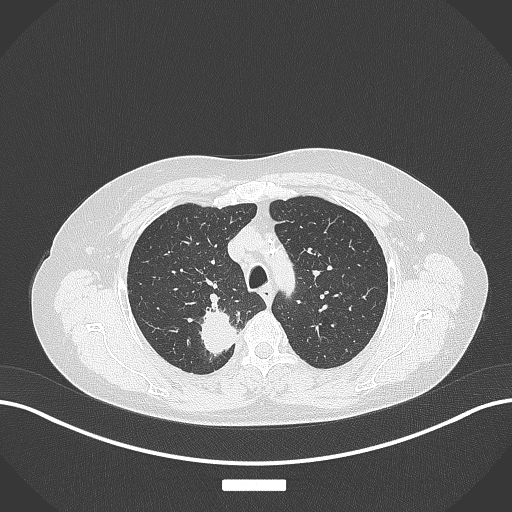
Chest CT, one axial slice. Position 298 of 357 along the scan axis. 120 kVp. Lung window (W 1500 / L -600 HU). 512 × 512 image matrix, field of view 400 × 400 mm. Patient: female, 62 years. From the clinical record (not read from this slice): clinical TNM (as recorded): T1c N1 M0.
Outlined on this slice (rectangle marked by the reading radiologist):
- lung tumour (recorded histology: squamous cell carcinoma): bounding box [x1, y1, x2, y2] px = [195, 298, 237, 360]